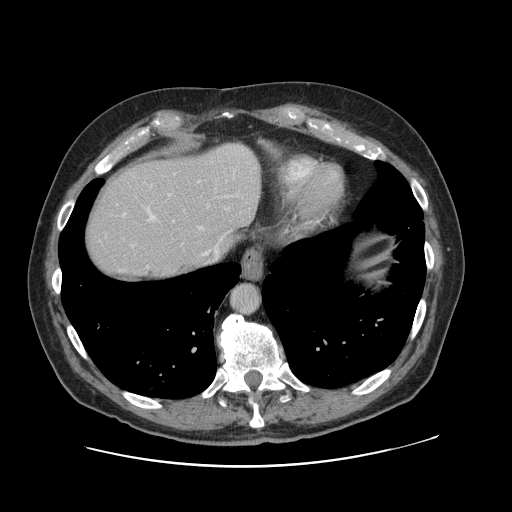
Contrast-enhanced abdominal CT, one axial slice; 120 kVp; soft-tissue window (W 400 / L 40 HU); 512 × 512 image matrix. Male patient, age 71 years. Case-level facts recorded for this patient, not image findings: diagnosis: colorectal cancer liver metastases, imaged before liver resection; multiple liver metastases: no; largest metastasis: 3.3 cm; disease in both lobes: no.
Outlined on this slice (expert manual segmentation):
- hepatic veins: bounding box (x1, y1, x2, y2) in pixels: (148, 210, 228, 265)
- liver: (85, 143, 261, 283)
- planned liver remnant (the part of the liver to remain after resection): (85, 163, 226, 283)